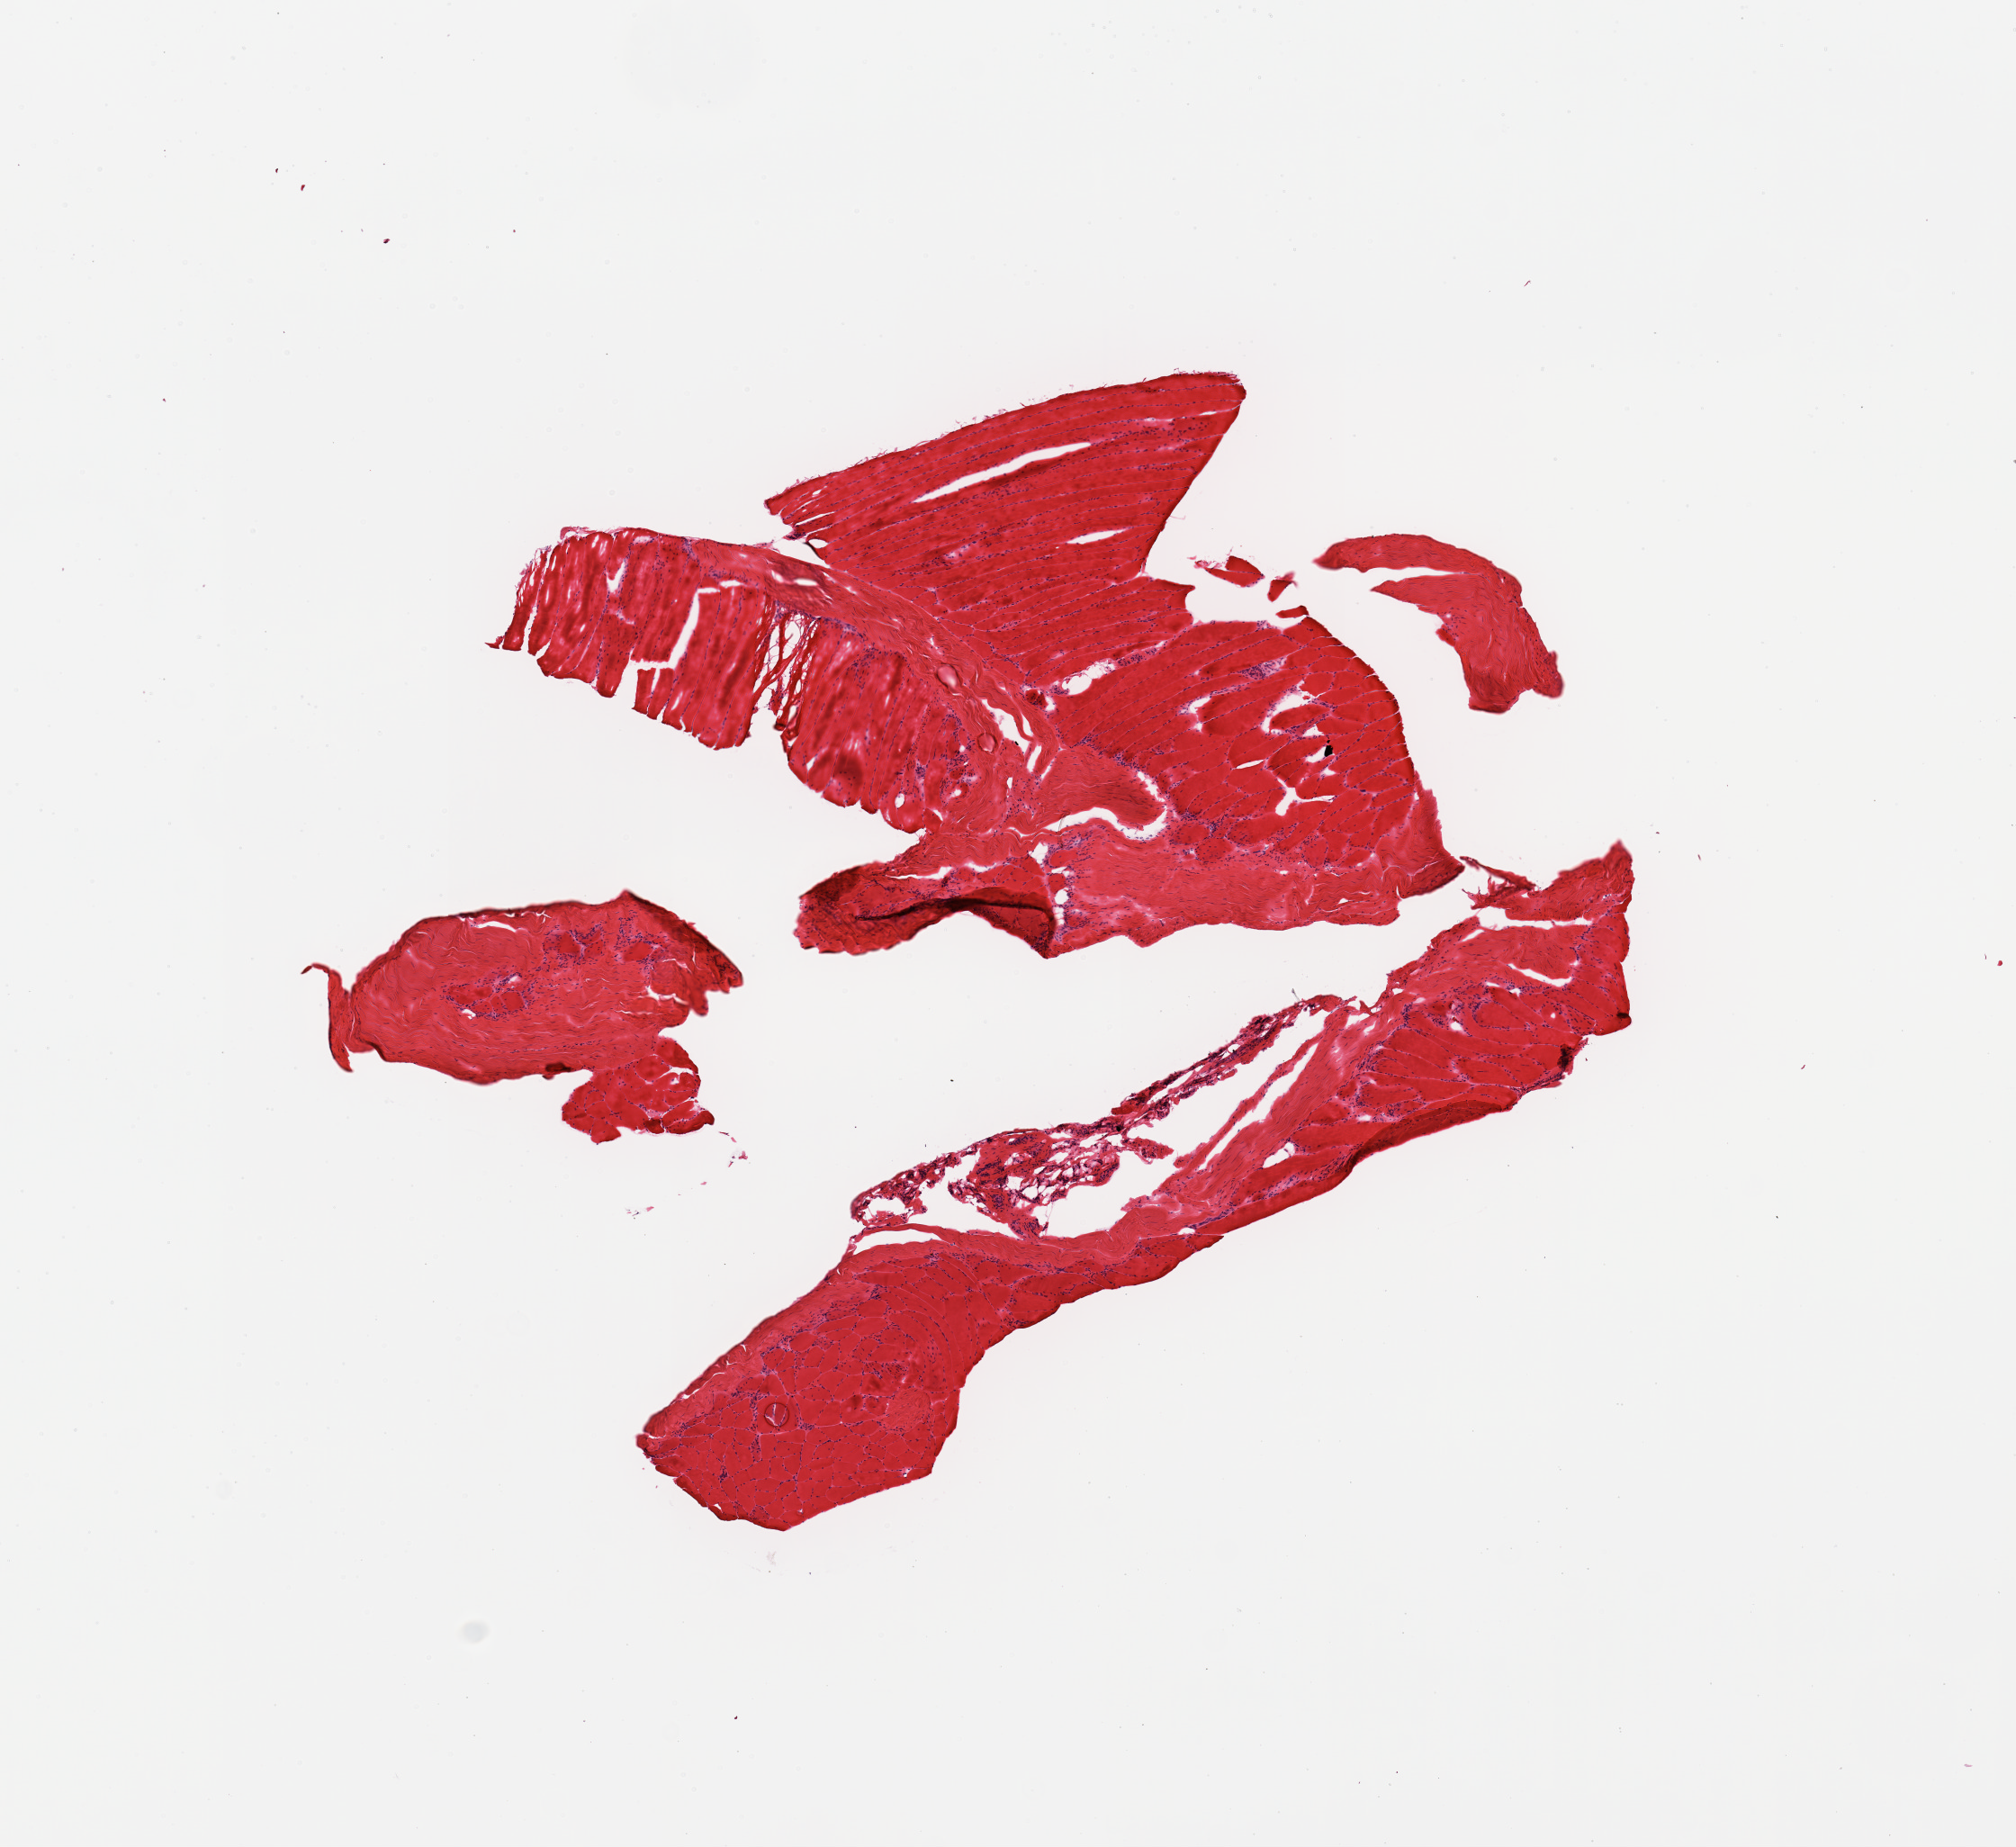
H&E whole-slide image, low-resolution overview of the scanned area, about 8.9 x 8.1 mm, frozen section (dry ice), sampled site (target tissue): skeletal muscle, donor tissue sample. Donor sex: male.
Reviewer comment on this tissue sample: 1 piece (fragmented), 10-20% fibrous tissue.